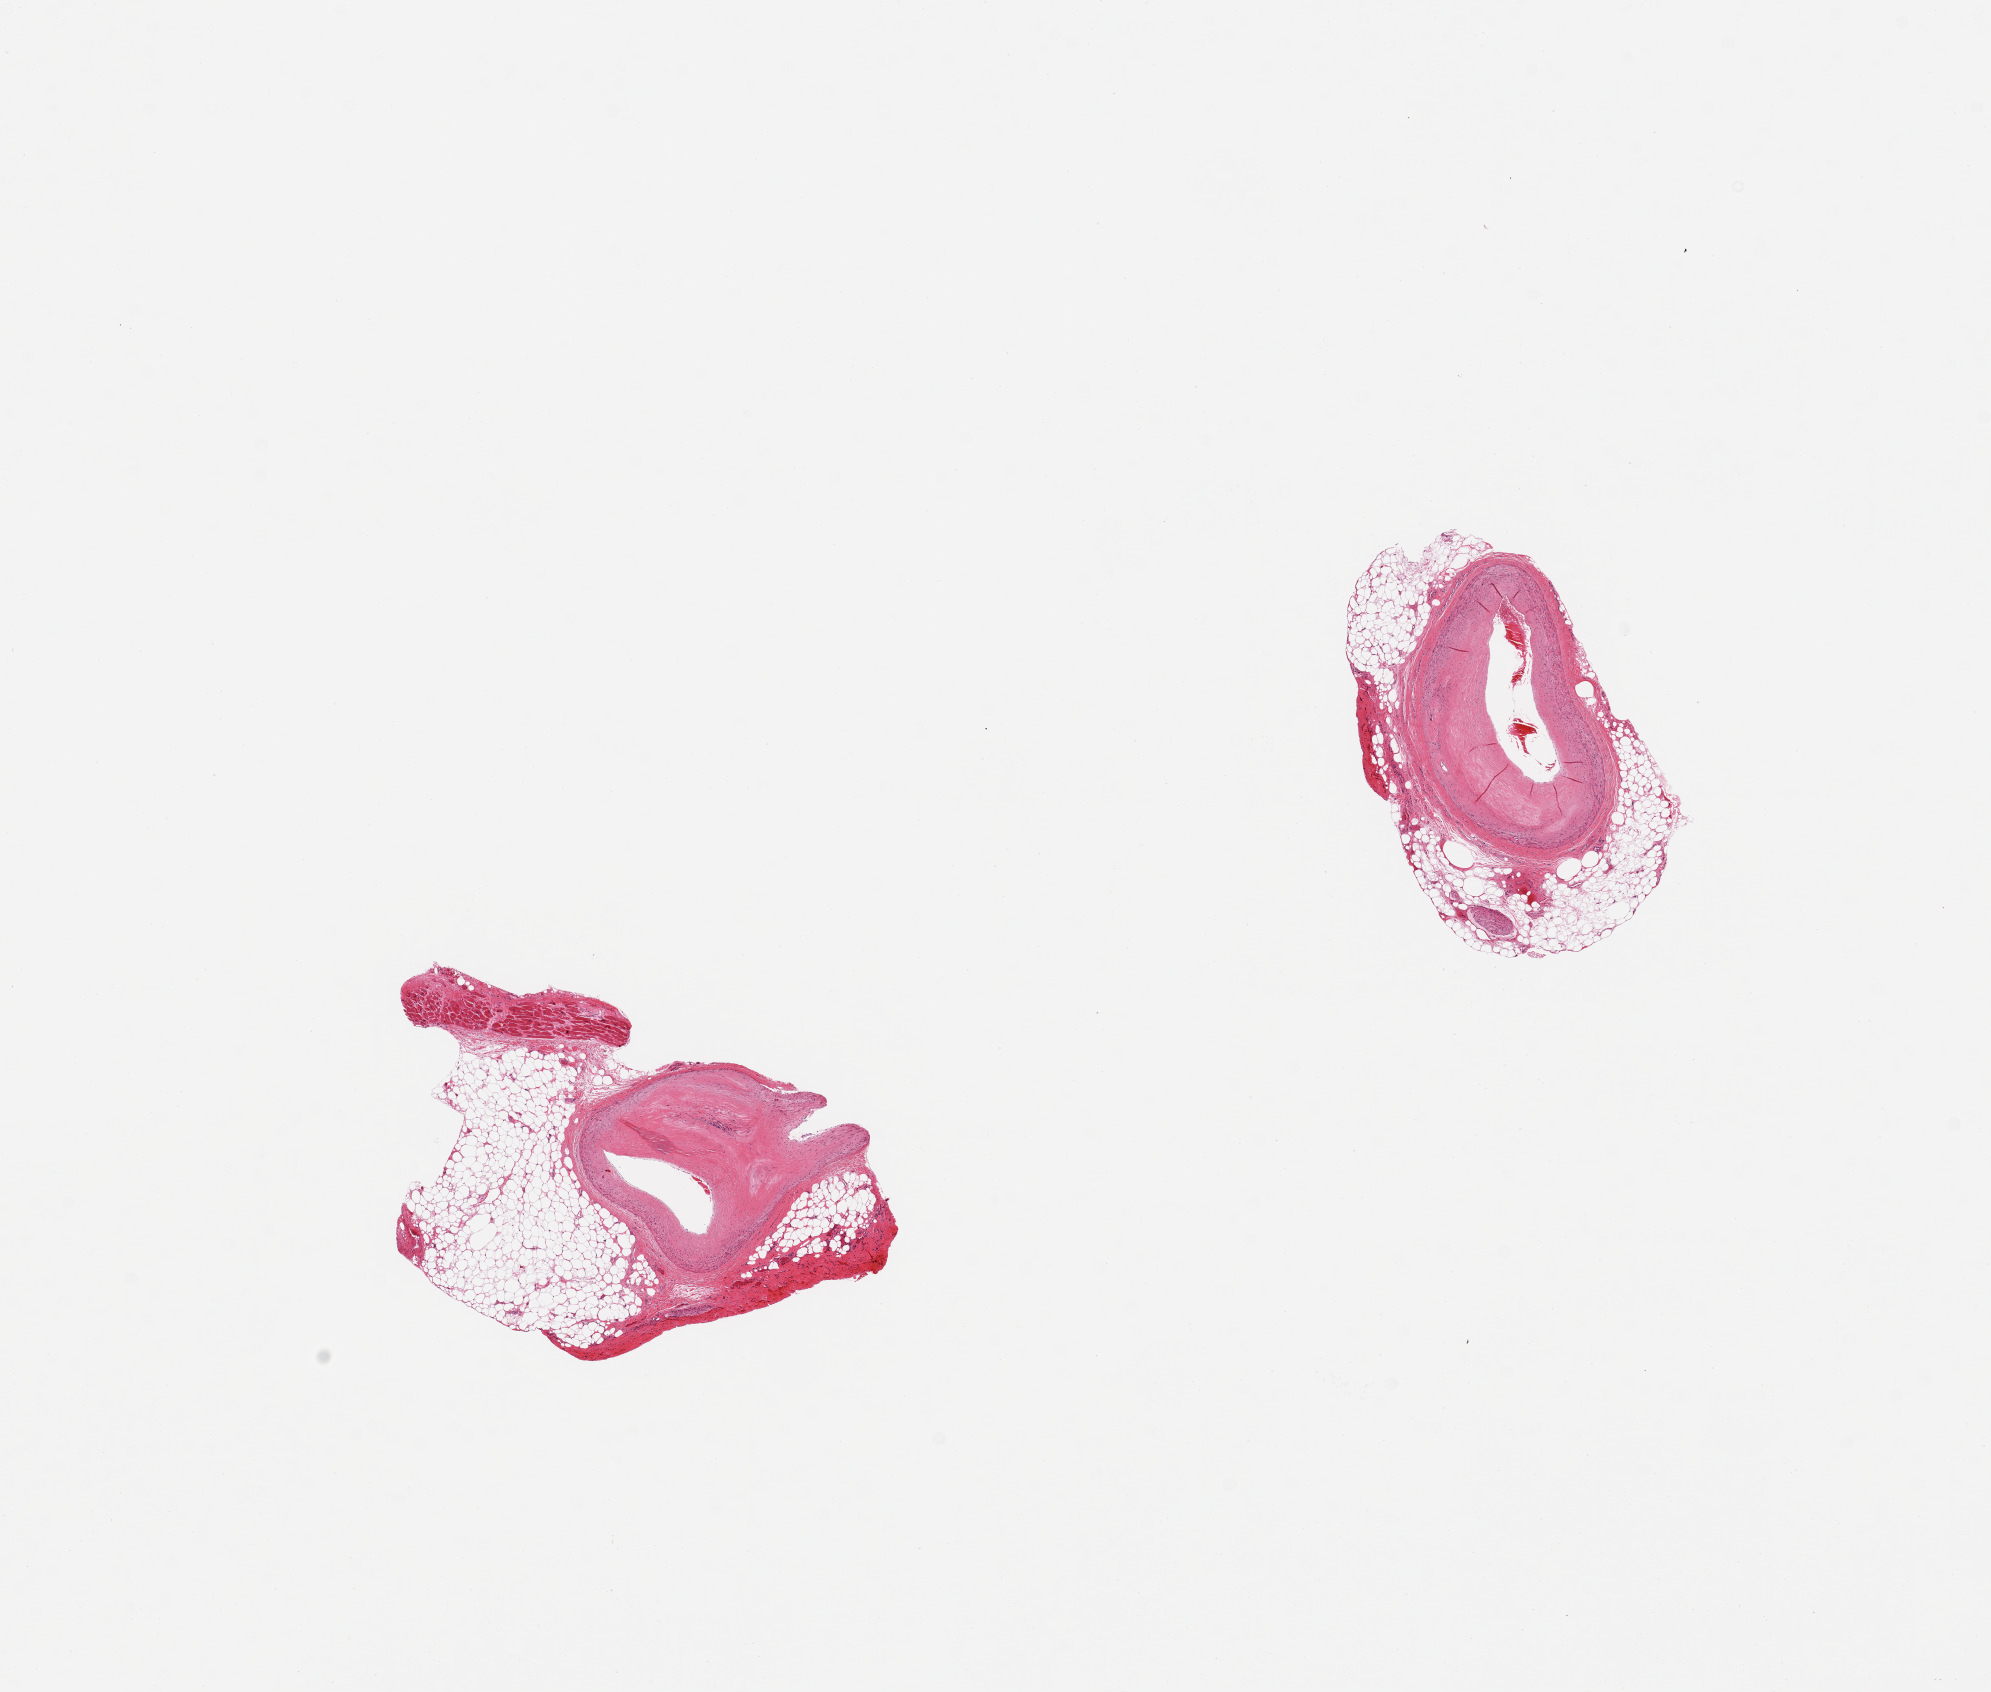
Whole-slide image, hematoxylin and eosin (H&E) stain — whole scanned area (about 15.8 x 13.4 mm) shown as a low-resolution overview, PAXgene-fixed paraffin-embedded (PFPE) section, target tissue: coronary artery, tissue donor sample. Donor sex: male.
Review note (as recorded): 2 pieces. Thick intimal plaques. 40 & 50% perivascular fat. 10% heart muscle on one.